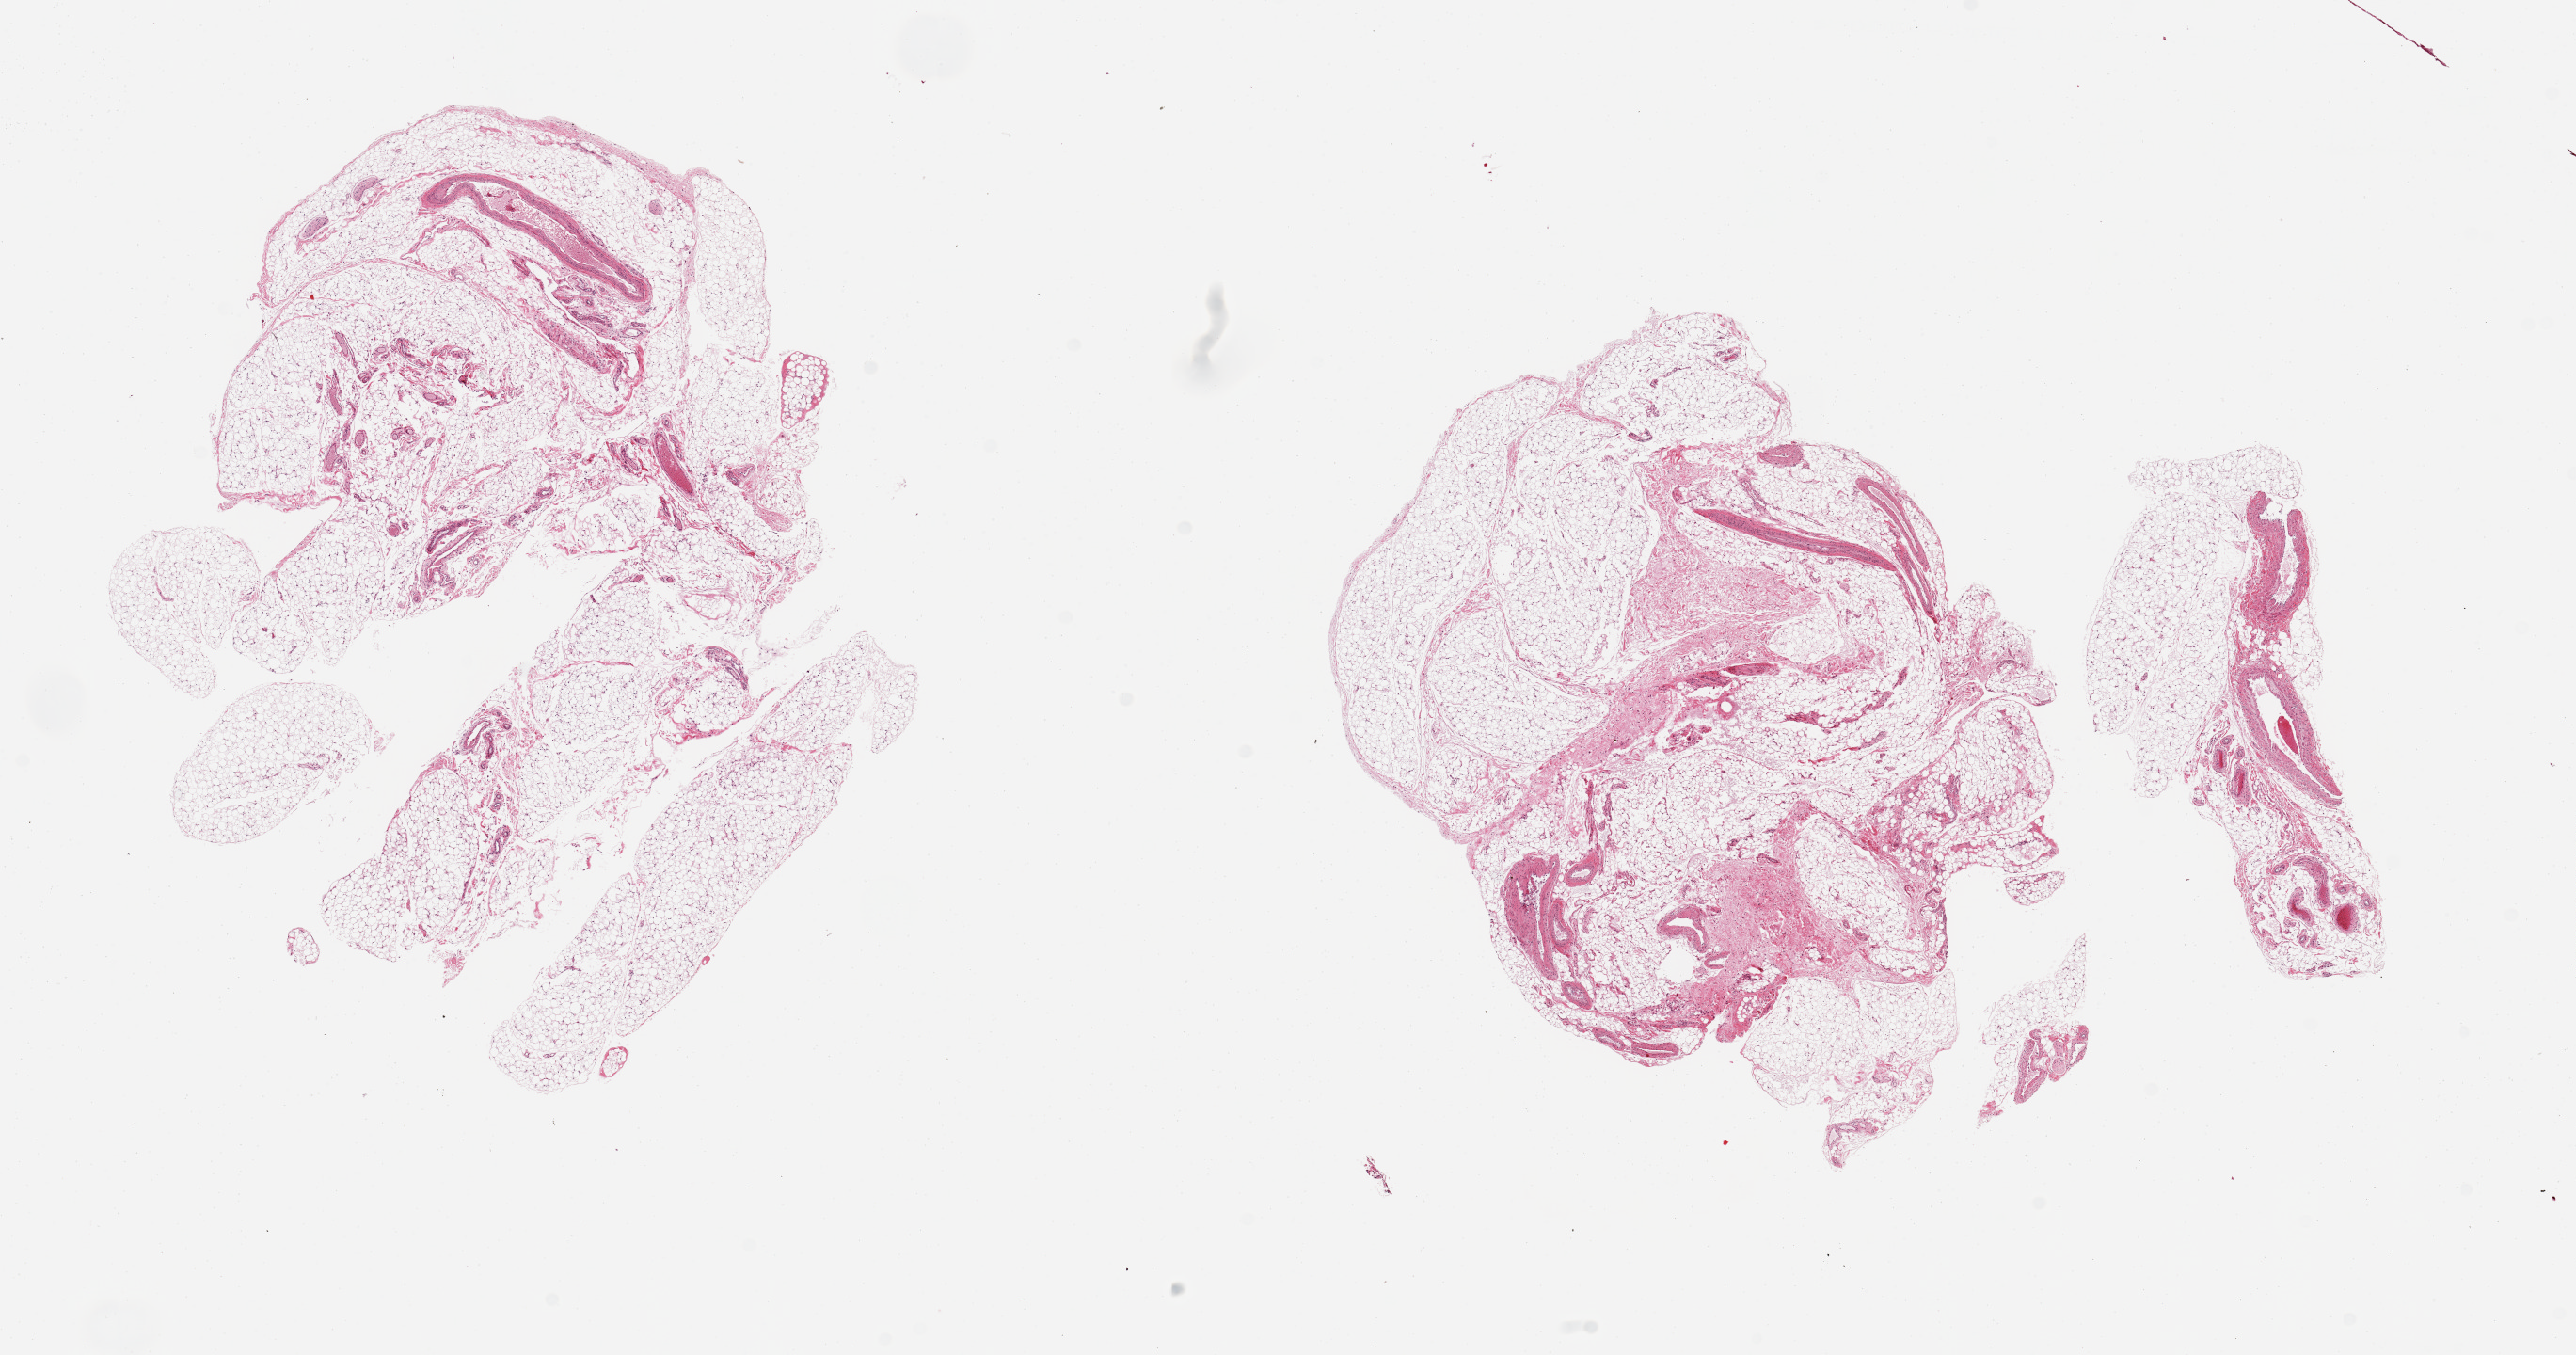
H&E whole-slide image — low-resolution overview of the scanned area, about 21.7 x 11.4 mm; PAXgene-fixed paraffin-embedded (PFPE) section; section of omentum (target tissue); tissue donor sample. Female donor.
Pathologist's review note for this sample: 2 pieces, ~10-15% vascular/fibrous tissue.